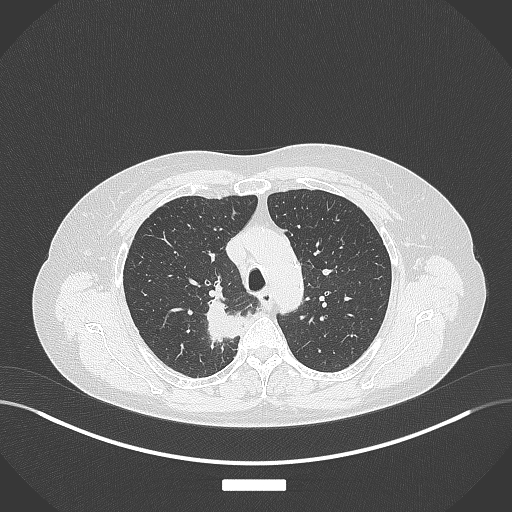
Chest CT, one axial slice; lung window (W 1500 / L -600 HU); 1 mm slice thickness; 512 × 512 image matrix, field of view 400 × 400 mm. Patient: female, 62 years. Case-level facts recorded for this patient, not image findings: clinical TNM (as recorded): T1c N1 M0.
Outlined on this slice (bounding box drawn by a radiologist):
- lung tumour (recorded histology: squamous cell carcinoma): box from (x=205, y=298) to (x=246, y=343) px